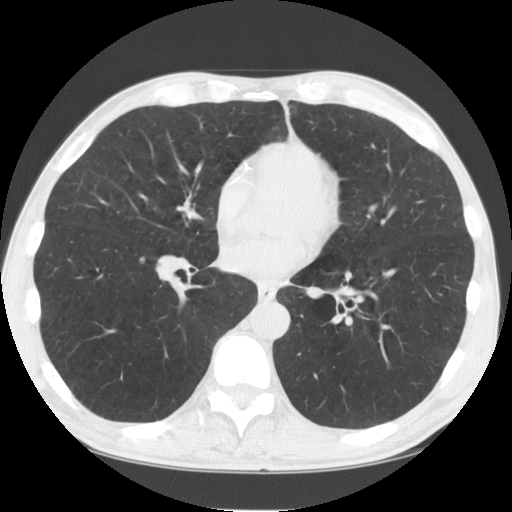
Axial slice from a low-dose chest CT screening exam; baseline screening round; lung window (W 1500 / L -600 HU); 2.5 mm slice thickness. Male, age 60 years at enrolment. Current smoker at enrolment.
- Lesion marked by an expert reader, bounding box (x1, y1, x2, y2) in pixels: (123, 244, 162, 273).
- No non-calcified nodule or mass ≥4 mm was recorded by the screening reader at this exam.
- Lung cancer was diagnosed 484 days after this screen (after the second annual screen): large cell carcinoma, NOS, right lower lobe, undifferentiated (G4), stage IA (AJCC 6th edition), 16 mm at pathology.